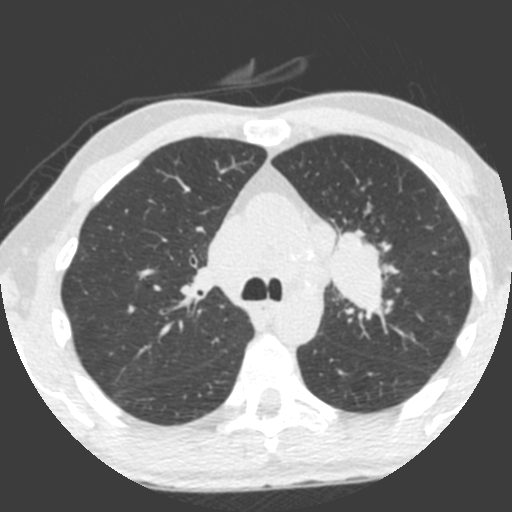
Low-dose screening chest CT, one axial slice. Position 148 of 212 along the scan axis. 120 kVp. Lung window (W 1500 / L -600 HU). 2 mm slice thickness. 512 × 512 image matrix, field of view 315 × 315 mm.
Structures marked on this image (outlined manually by an expert reader):
- lesion 1 (tumor, upper lobe of left lung): bounding box (x1, y1, x2, y2) in pixels: (329, 229, 384, 316)